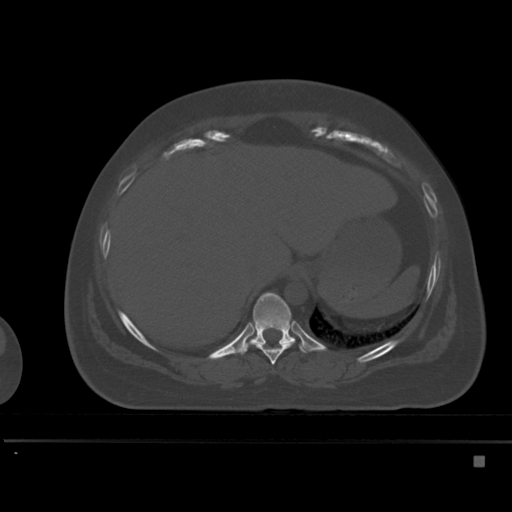
CT including the spine, one axial slice. Position 255 of 495 along the scan axis. Bone window (W 1800 / L 400 HU). 1.5 mm slice thickness. 512 × 512 image matrix. Patient: female, 33 years. From the clinical record (not read from this slice): primary cancer: breast; vertebrae with lytic lesions (as recorded): T1.
Structures marked on this image (semi-automatic segmentation, software-assisted and operator-edited):
- T10 vertebra: box from (x=238, y=292) to (x=307, y=355) px
- T9 vertebra: (x=253, y=341)–(x=296, y=365)